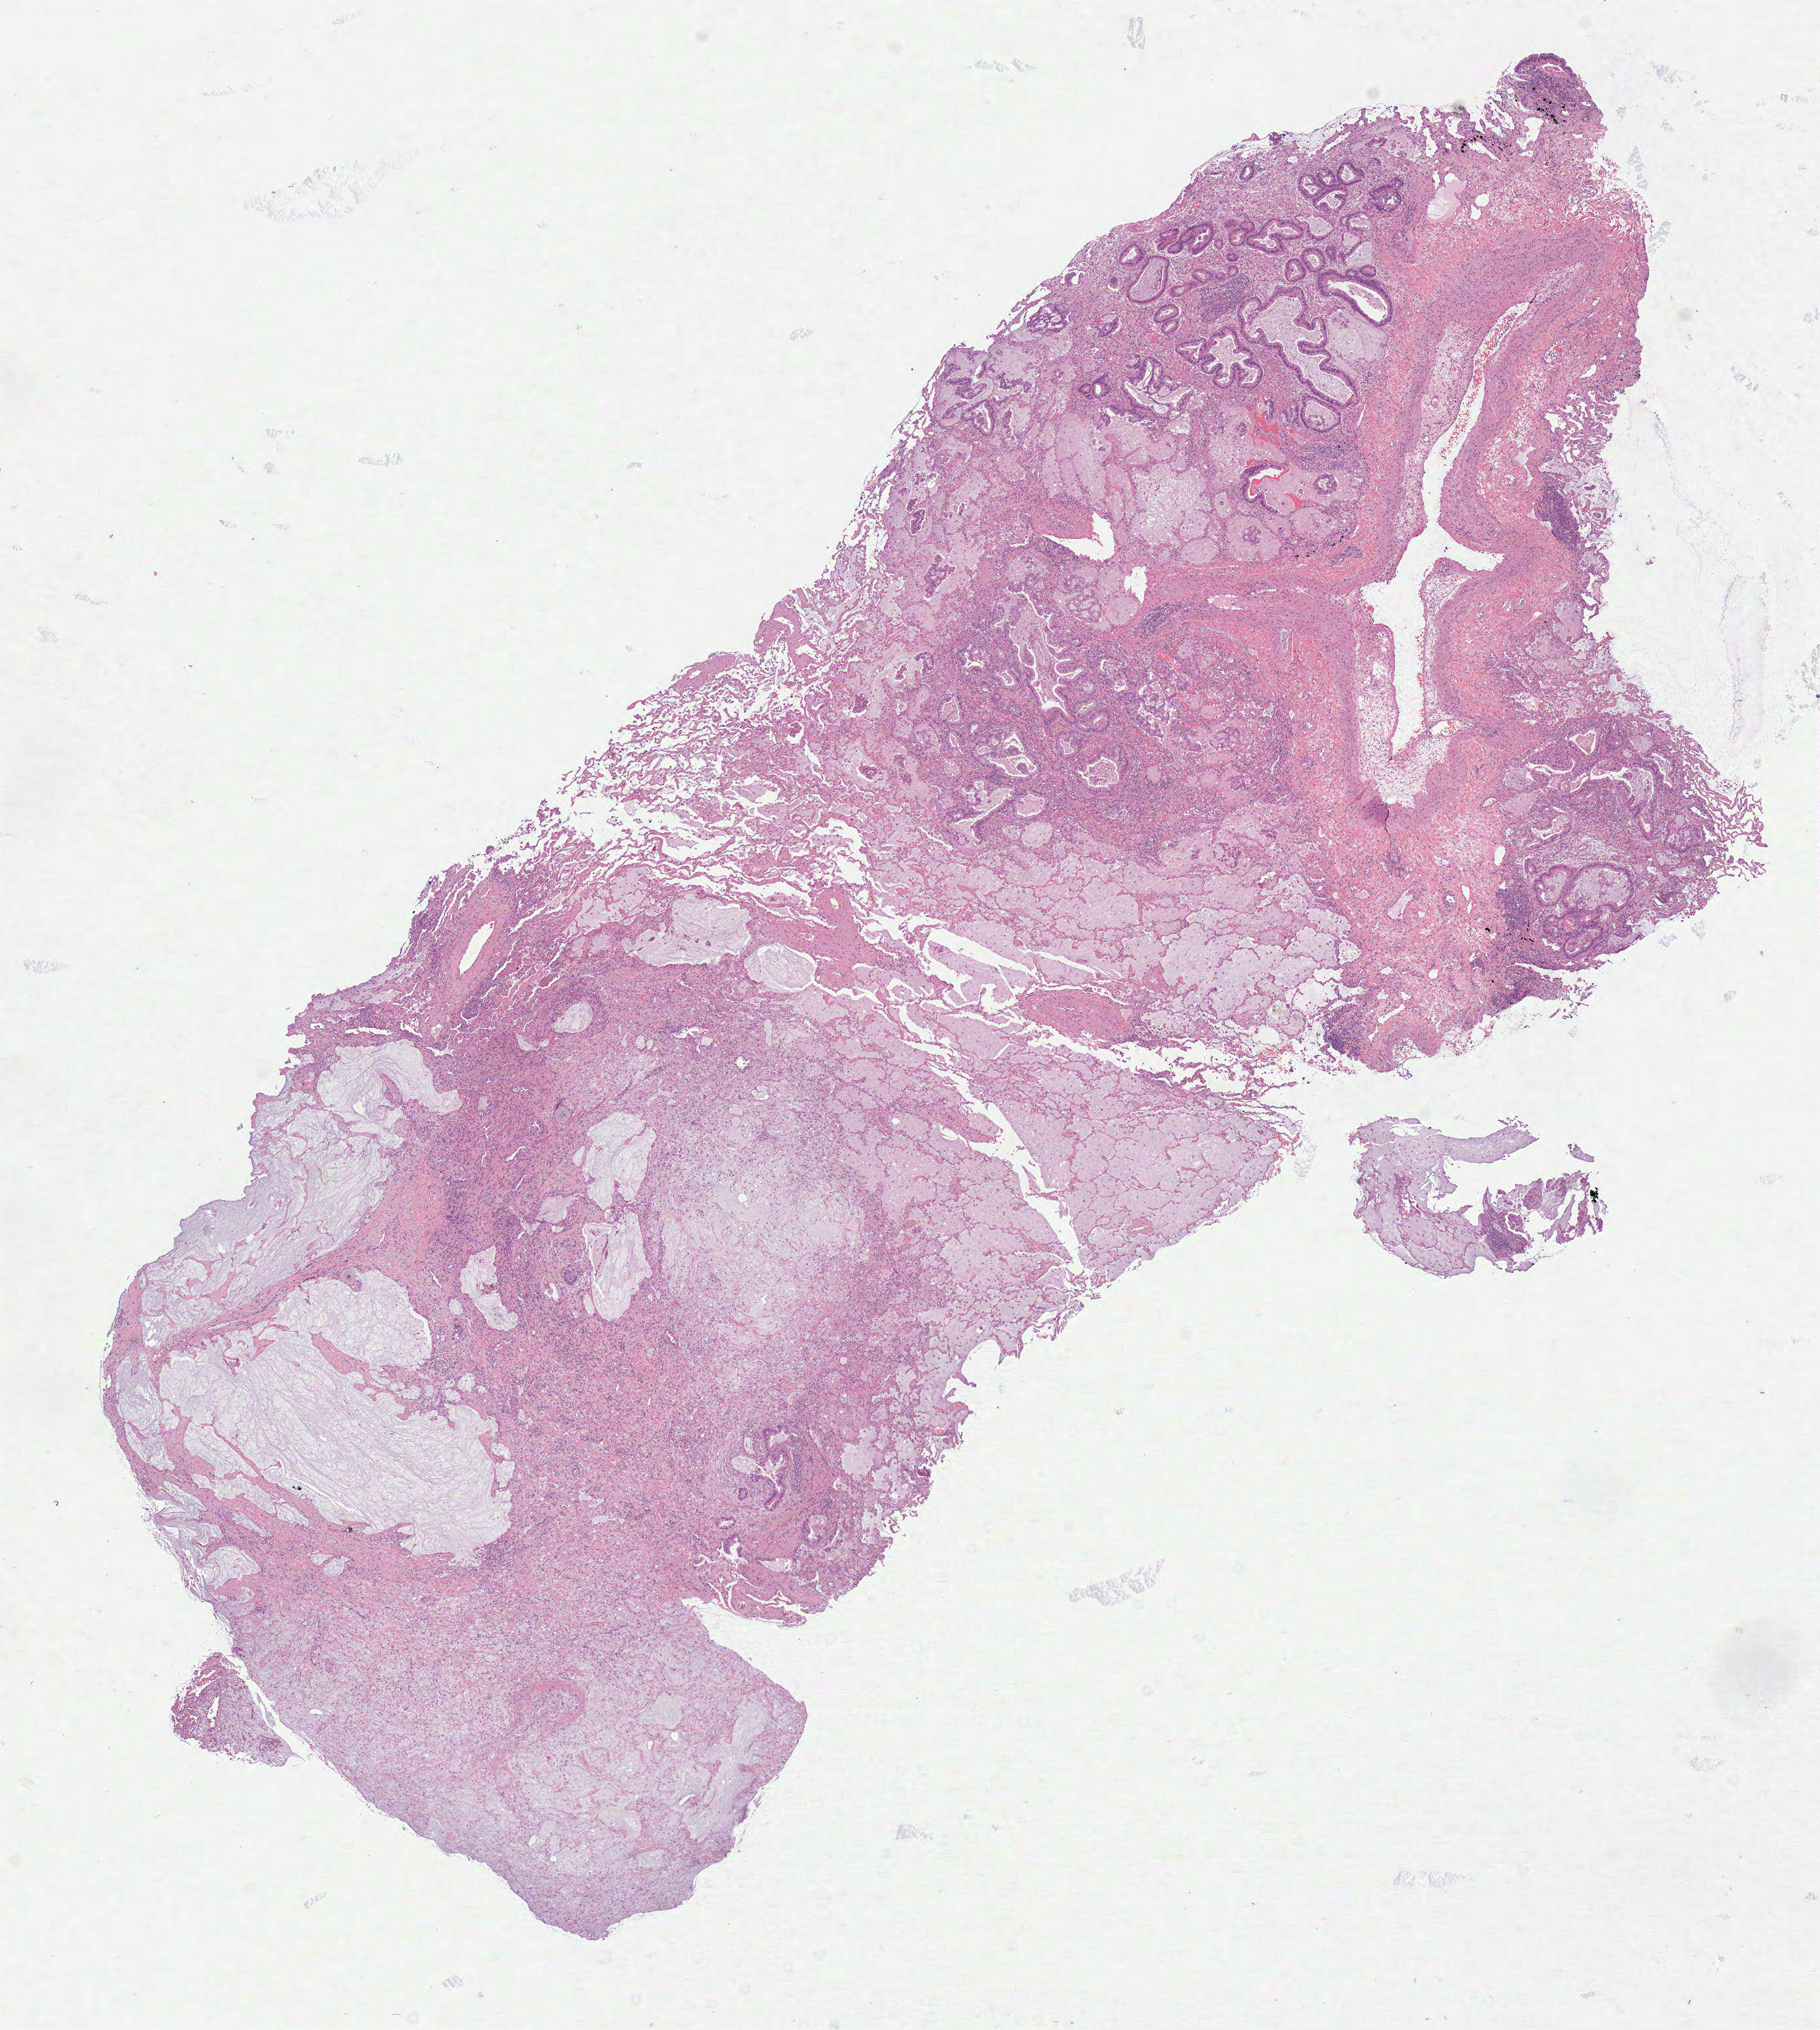
Hematoxylin and eosin (H&E) stained whole-slide image — whole scanned area (about 11.1 x 12.4 mm, acquisition: 40x scan) shown as a low-resolution overview. Formalin-fixed paraffin-embedded (FFPE) diagnostic section. Primary tumour sample from the lung. Male patient; age at initial diagnosis 81 years.
AJCC pathologic stage: IIB (6th edition). Laterality: left. Histologic diagnosis: Mucinous adenocarcinoma (lower lobe, lung).